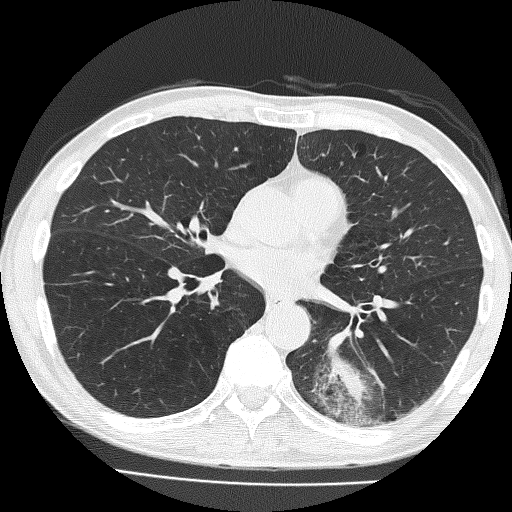
Low-dose screening chest CT, axial slice. Baseline screening round. Lung window (W 1500 / L -600 HU). 2 mm slice thickness. Lung (sharp) reconstruction kernel (FC51). Slice 83 of 160 in the series. 512 × 512 image matrix. Male participant, aged 58 years at enrolment. Current smoker at enrolment.
• Expert reader's lesion annotation, bounding box <304,315,418,433> (left, top, right, bottom; pixels).
• The screening reader recorded 2 non-calcified nodules or masses ≥4 mm on this exam (left lower lobe, left upper lobe); which of them this box marks is not recorded.
• Lung cancer was diagnosed 39 days after this screen: non-small cell carcinoma, left lower lobe, poorly differentiated (G3), stage IV (AJCC 6th edition), 74 mm at pathology.